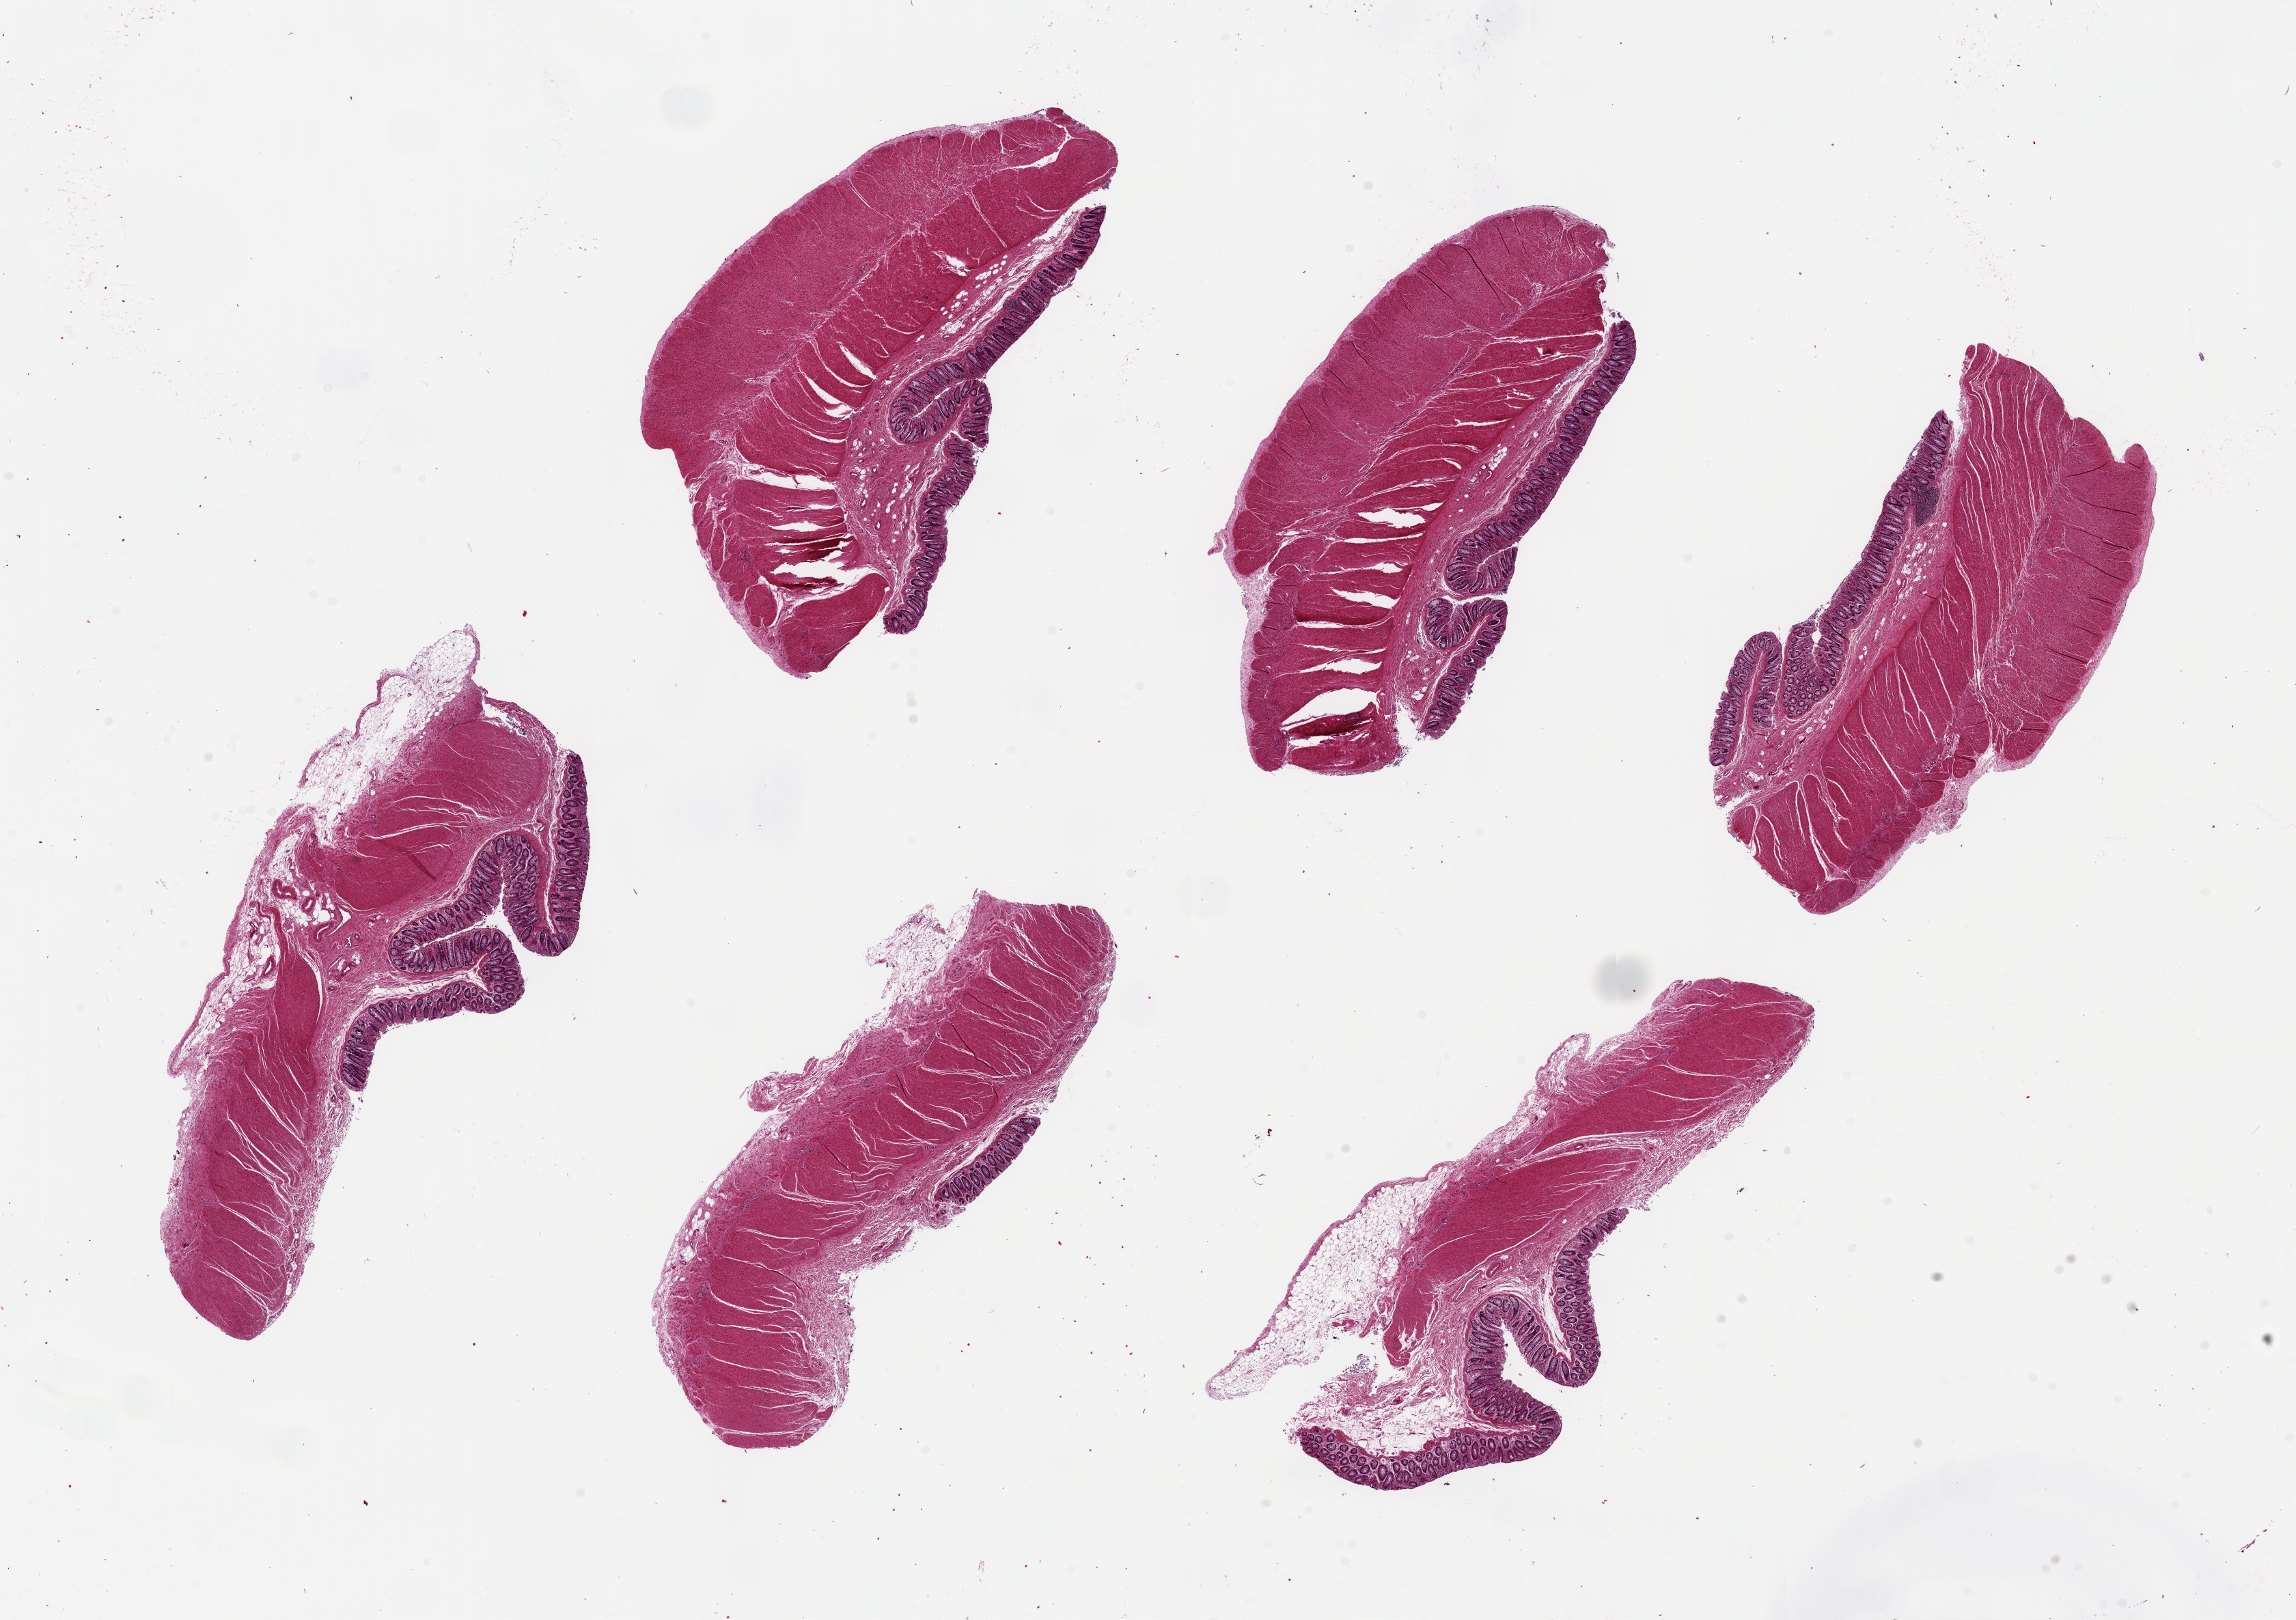
Whole-slide image, H&E stain, whole scanned area (about 26.6 x 18.8 mm, slide scanned at 20x) shown as a low-resolution overview; PAXgene-fixed paraffin-embedded (PFPE) section; sampled site (target tissue): sigmoid colon; tissue donor sample. Donor sex: female.
Review note (as recorded): 6 pieces, up to 8.5x4mm; ~90% muscle/fat, rest is well preserved mucosa.